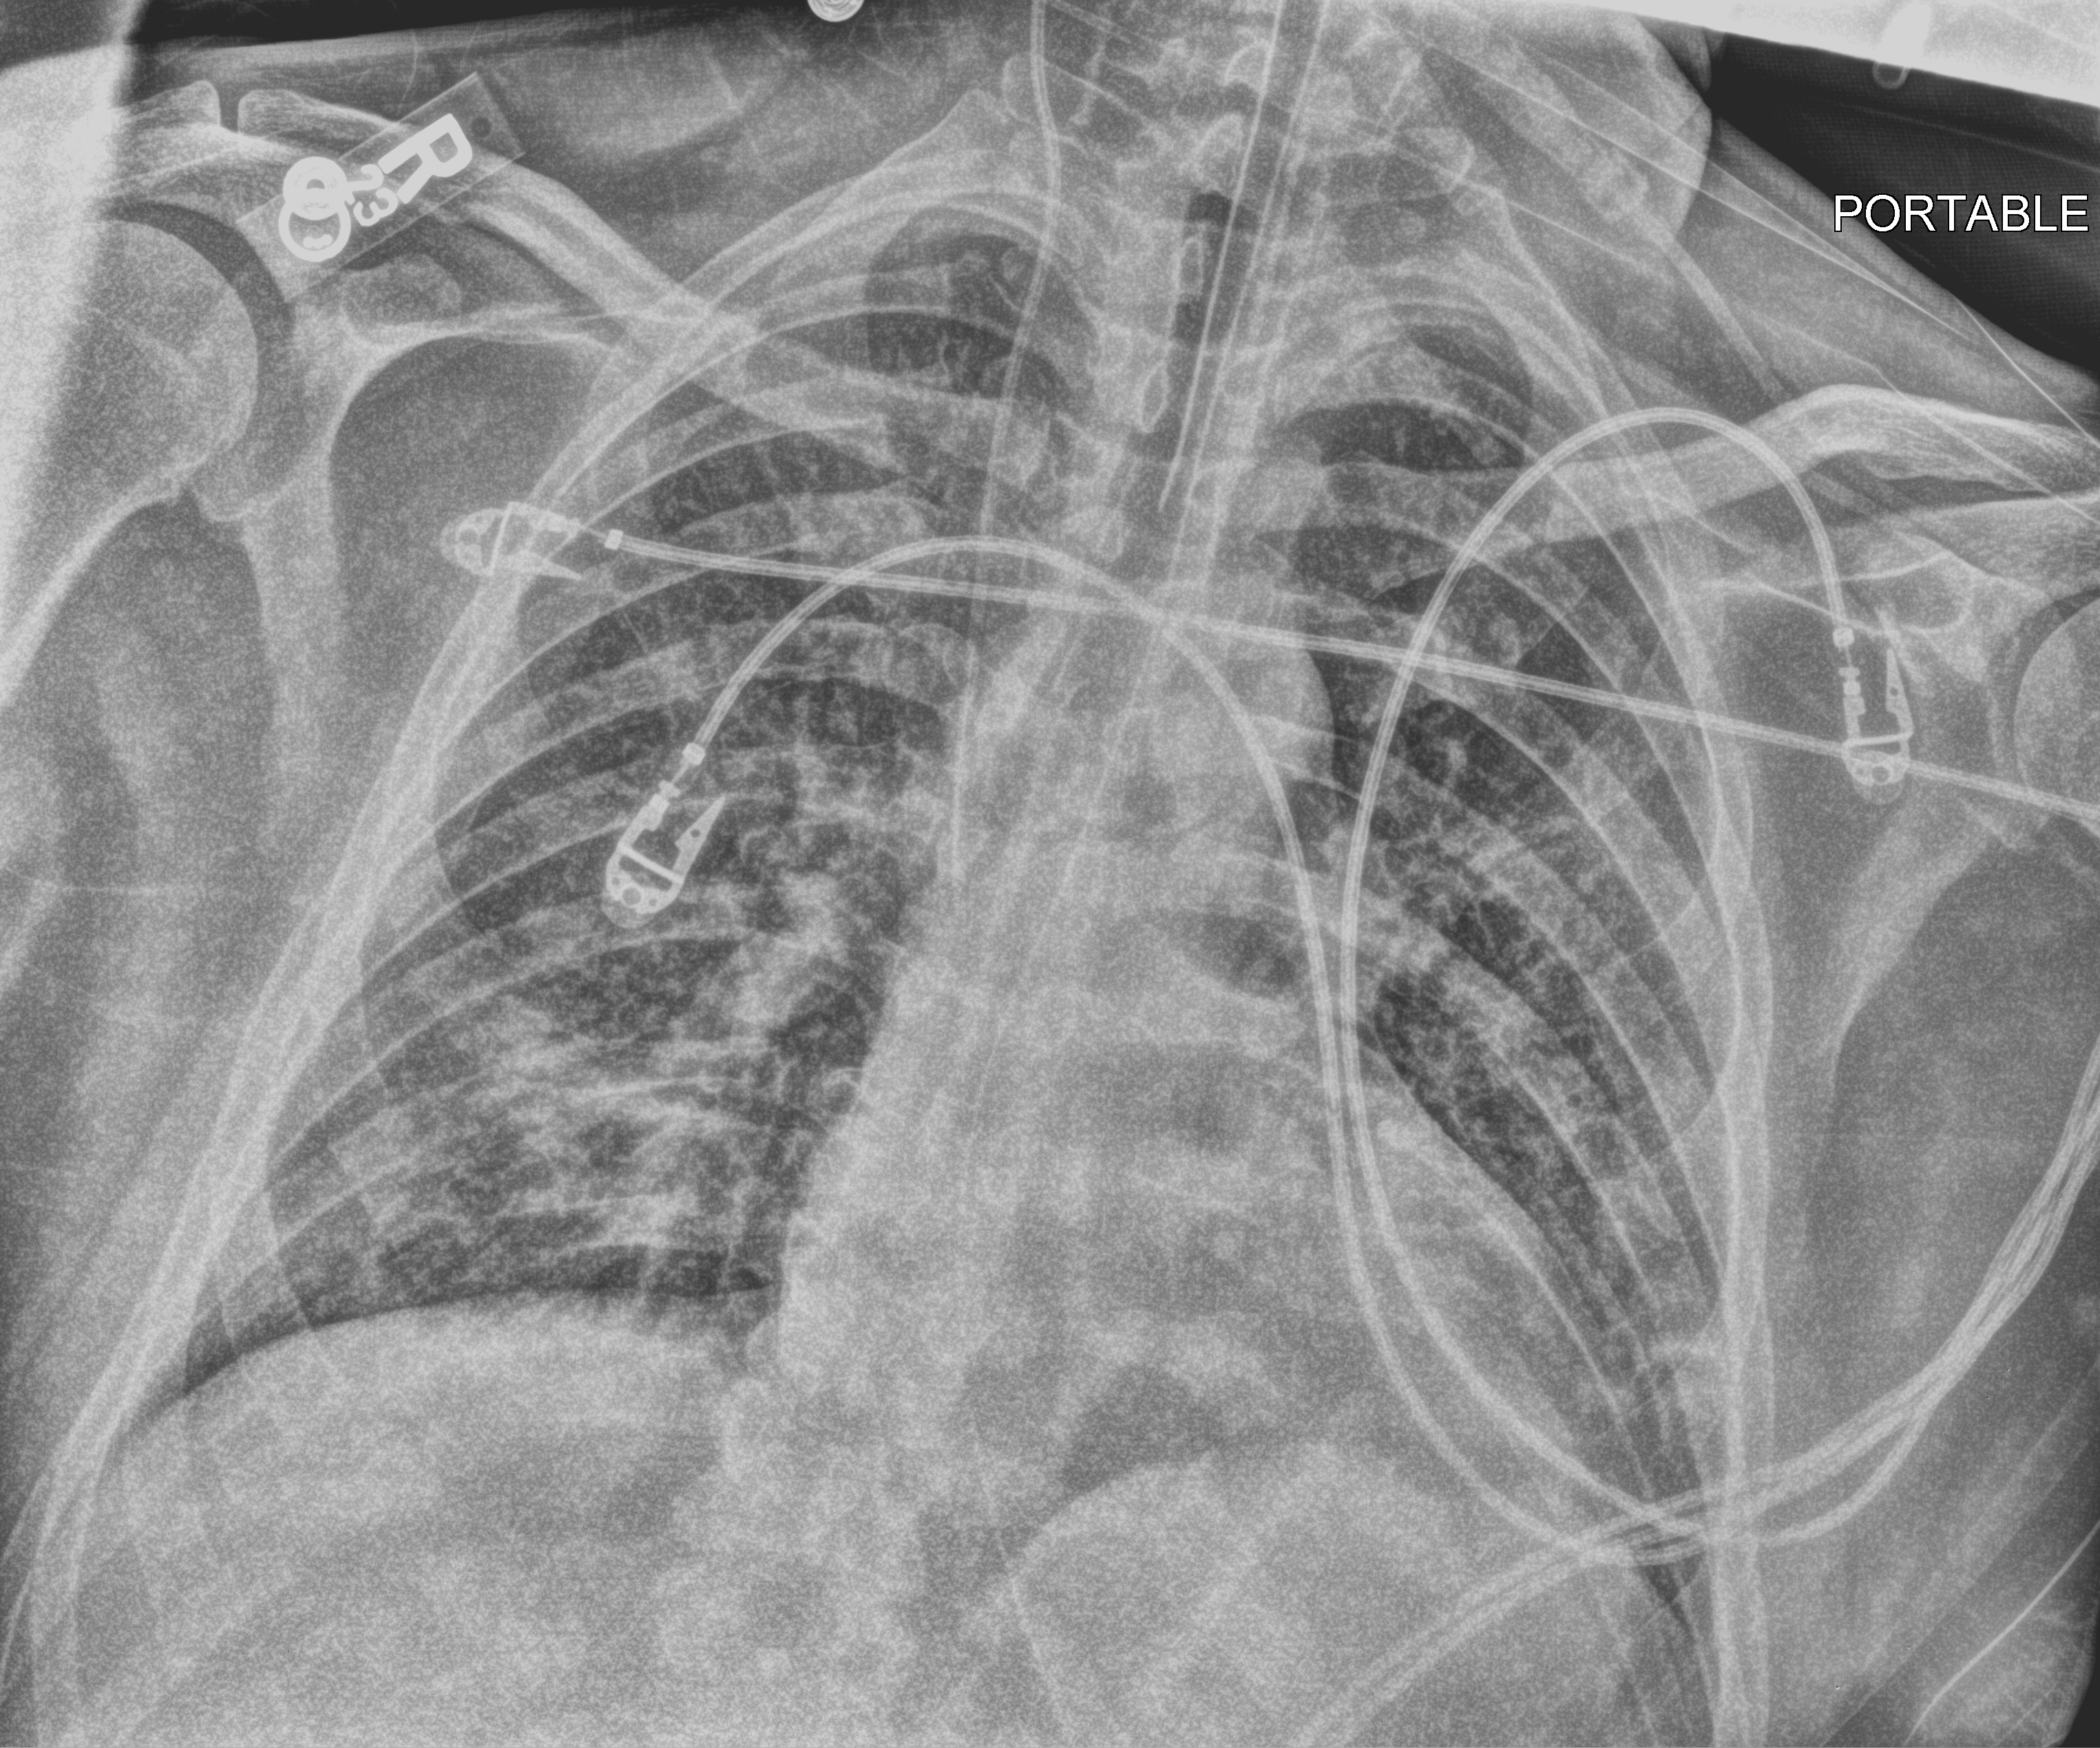
Portable chest radiograph; anteroposterior (AP) projection. Patient hospitalised with COVID-19; male, aged 18–59 years.
Hospital-stay facts (about this admission, not read from this image; timing relative to this image not recorded):
- admitted to intensive care during this hospital stay: no
- mechanically ventilated during this hospital stay: yes